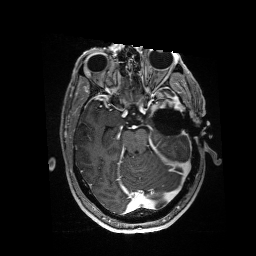
Brain MRI from a brain-tumour surgery series, one axial slice; position 104 of 176 along the scan axis; T1-weighted post-contrast; 1 mm slice thickness; 256 × 256 image matrix, field of view 256 × 256 mm. From the clinical record (not read from this slice): histopathology: Glioblastoma; WHO grade: 4; IDH mutation: no; tumour location: Left Anterior/Superior Temporal.
Annotated regions visible in this slice (manually delineated by an expert):
- residual tumour: bounding box <151,93,185,113> (left, top, right, bottom; pixels)